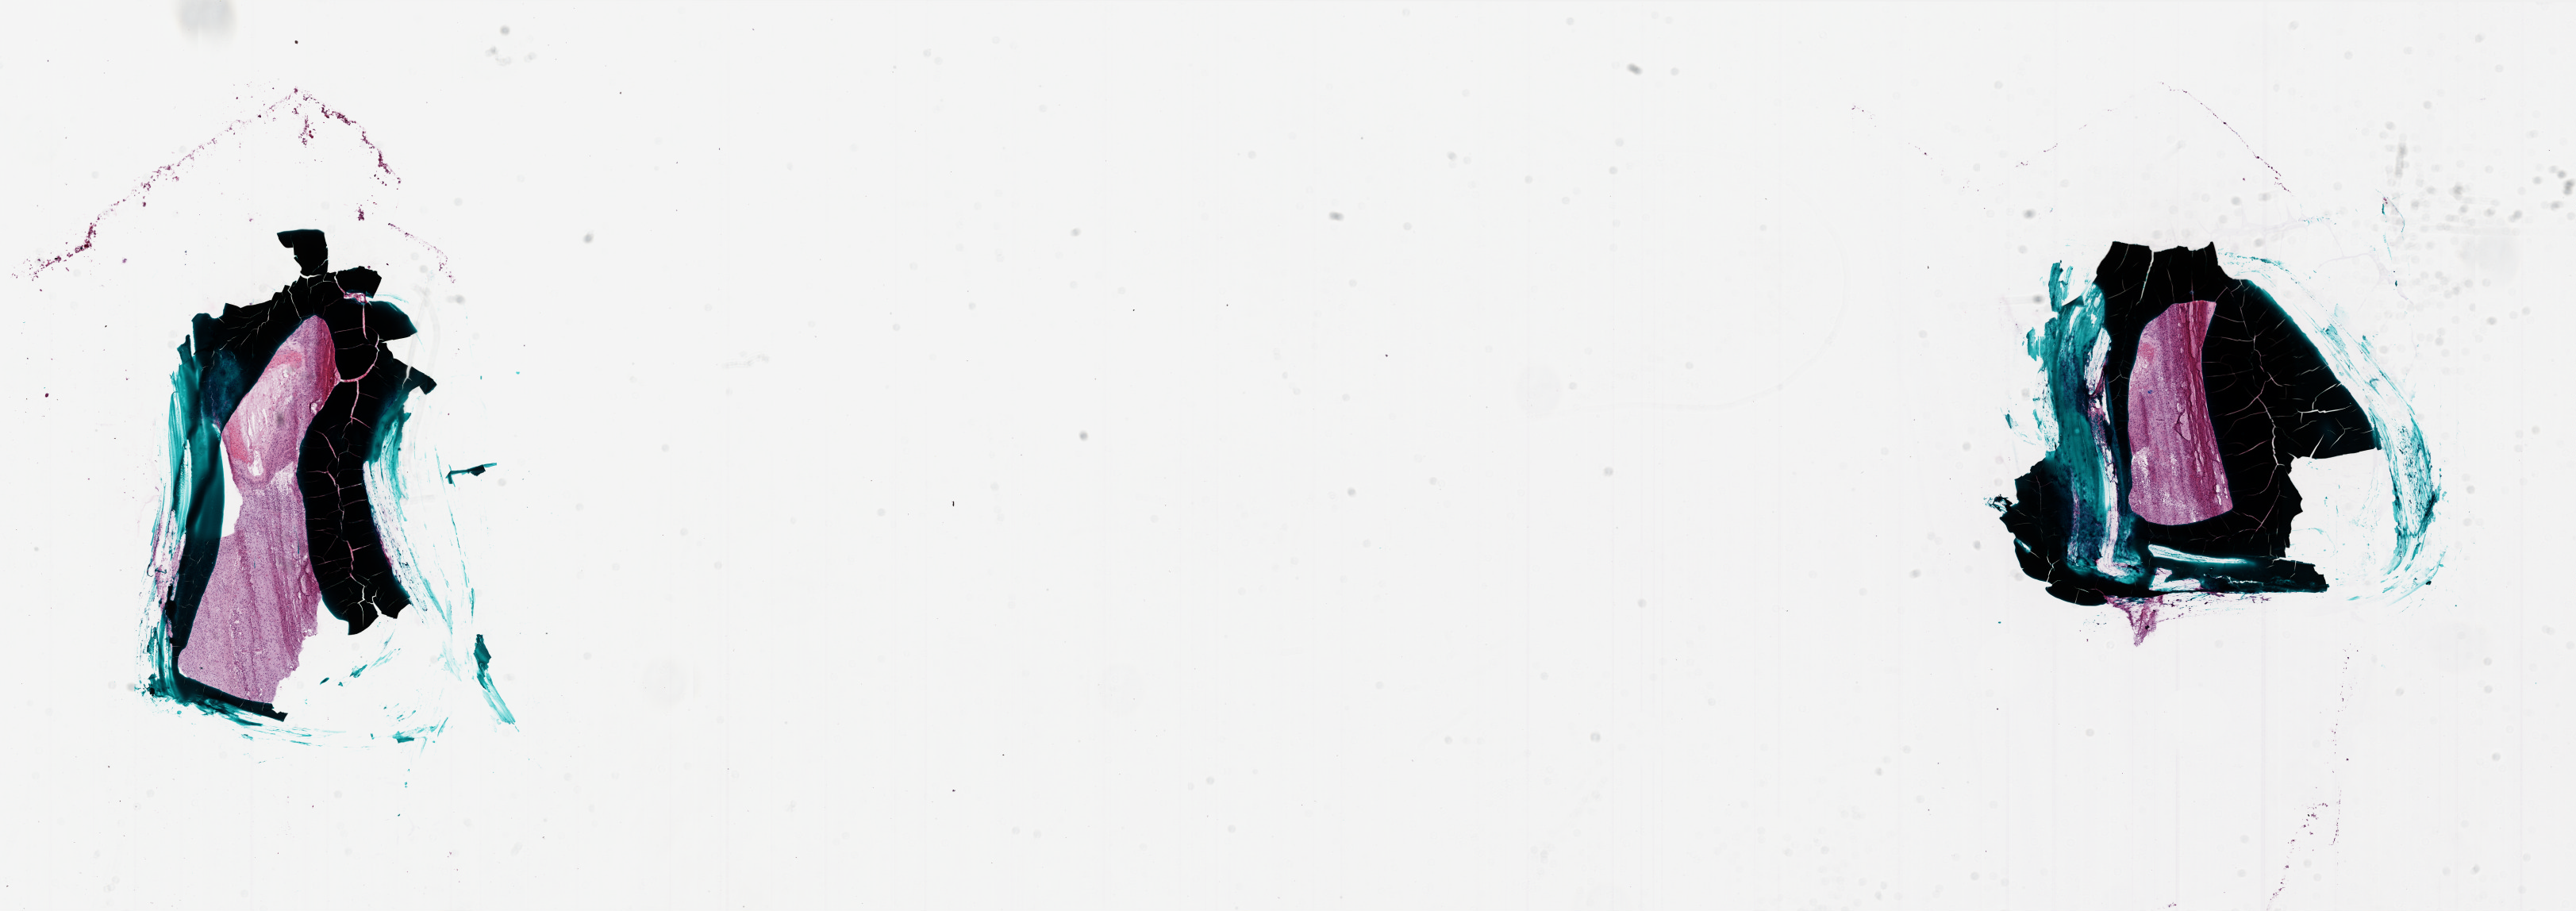
H&E whole-slide image — a low-resolution overview of the entire scanned area, about 26.0 x 9.2 mm (acquisition: 20x scan), frozen section from the bottom of the tissue portion, primary tumour sample from the brain. Male, age 69 years at initial diagnosis. Slide review estimates, as recorded: tumour cells 80%, tumour nuclei 90%, normal cells 0%, stromal cells 20%, necrosis 0%.
Diagnosis: Glioblastoma.